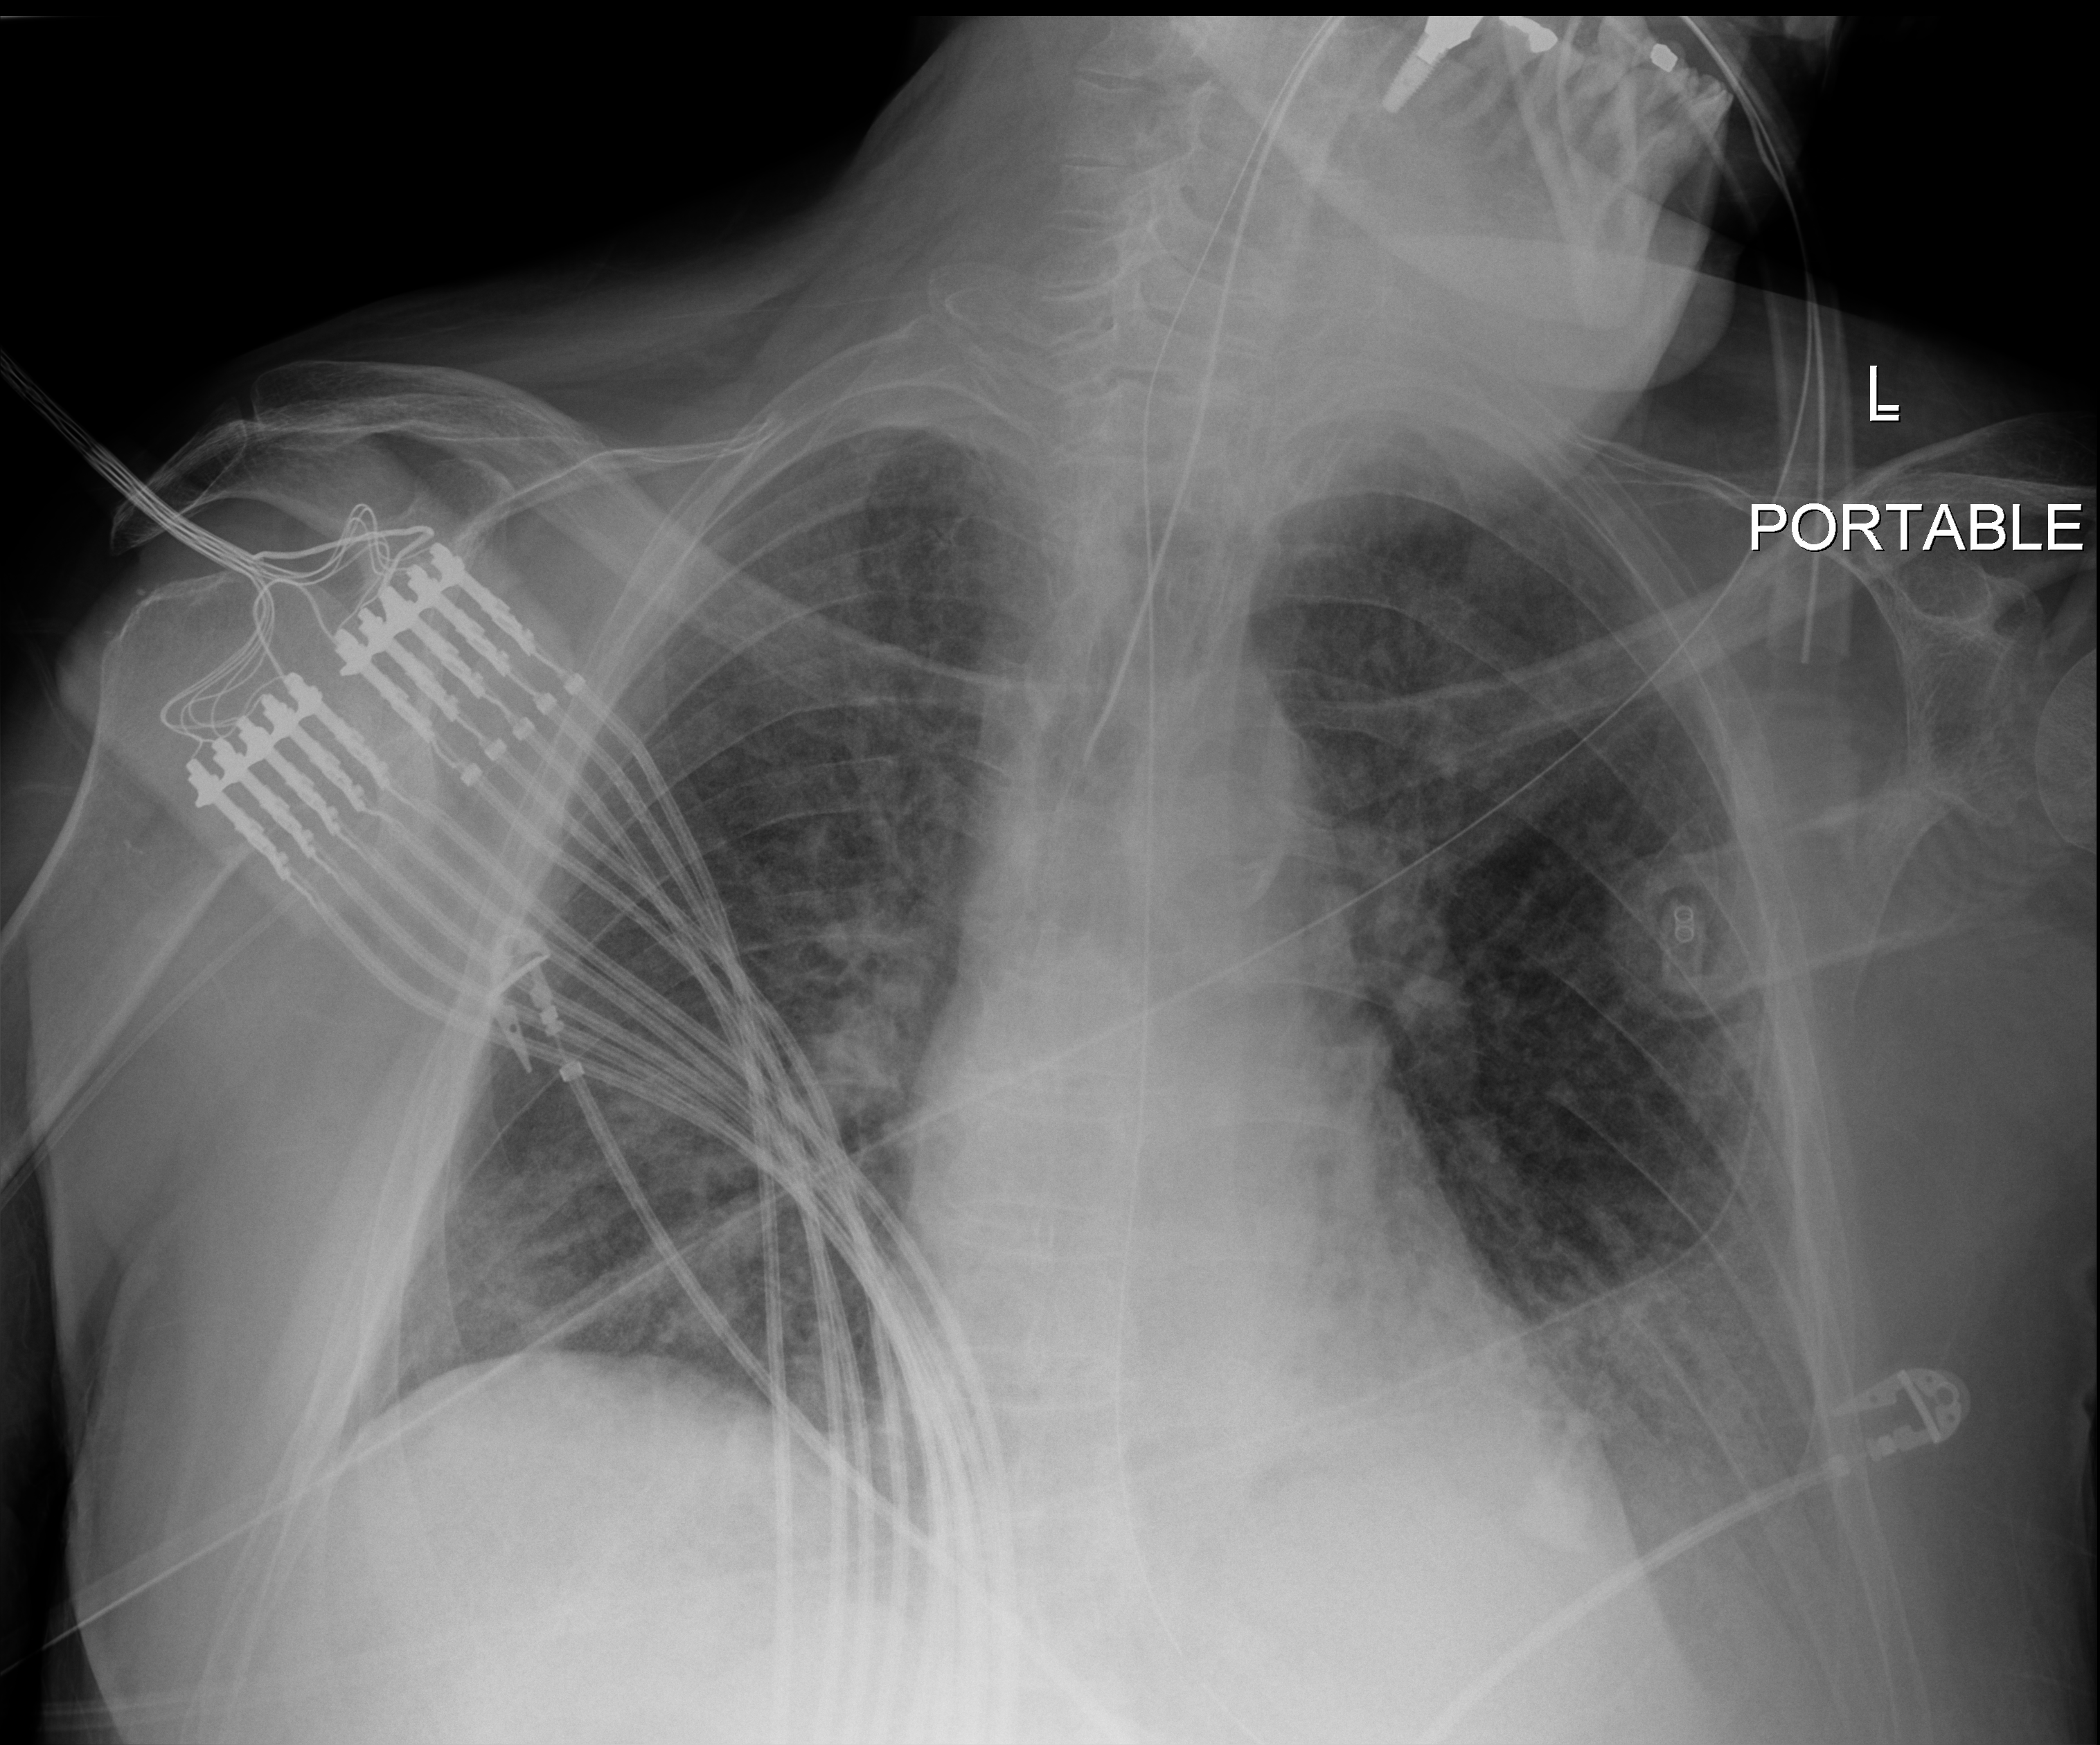
Portable chest radiograph, anteroposterior (AP) projection. Male patient hospitalised with COVID-19, age 60–74 years.
Admission-level facts for this patient (not findings on this image; timing relative to this image not recorded):
- length of hospital stay: 25 days
- admitted to intensive care during this hospital stay: yes